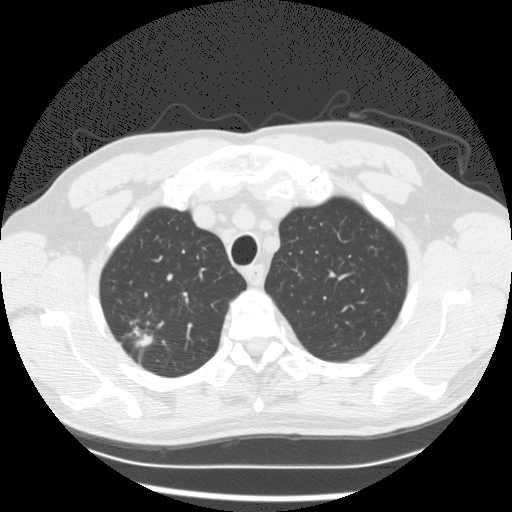
Low-dose screening chest CT, one axial slice. Reconstruction kernel STANDARD. 120 kVp. Lung window (W 1500 / L -600 HU). 2.5 mm slice thickness. 512 × 512 image matrix, field of view 351 × 351 mm.
Annotated regions visible in this slice (manually delineated by an expert):
- lesion 1 (tumor, upper lobe of right lung): bounding box <136,333,152,347> (left, top, right, bottom; pixels)